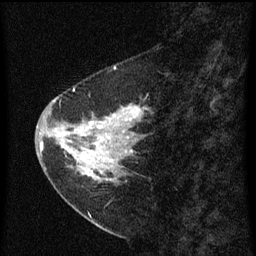
Breast MRI (dynamic contrast-enhanced), one sagittal slice; position 22 of 60 along the scan axis; dynamic contrast-enhanced series, image 2 of 3 at this slice position (ordered by acquisition); 1.5 T; TE 4.2 ms, TR 8 ms; 2 mm slice thickness; 256 × 256 image matrix. Female patient, age 47 years.
Annotated regions visible in this slice (semi-automatically segmented with operator editing):
- analysis volume of interest (the breast-tissue region the enhancement analysis was run in; not a lesion): bounding box (x1, y1, x2, y2) in pixels: (44, 84, 149, 199)
- tumour enhancement mask (voxels above the 70 % enhancement threshold inside the analysis volume of interest): (44, 90, 147, 175)